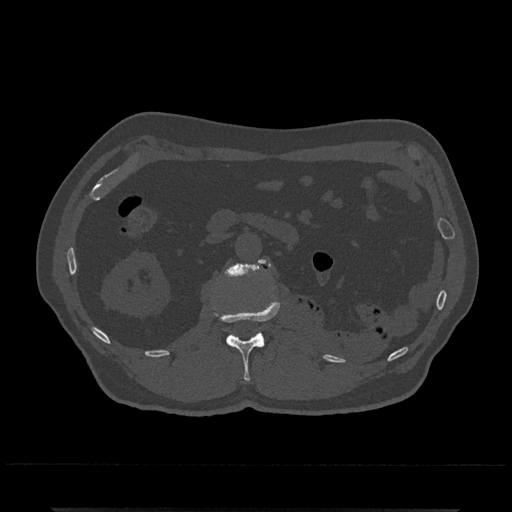
CT including the spine, one axial slice; position 340 of 797 along the scan axis; 120 kVp; bone window (W 1800 / L 400 HU); 0.5 mm slice thickness; 512 × 512 image matrix, field of view 393 × 393 mm. Patient: male, 67 years. Case-level facts recorded for this patient, not image findings: primary cancer: prostate.
Structures marked on this image (semi-automatically segmented with operator editing):
- L1 vertebra: box from (x=214, y=301) to (x=280, y=381) px
- L2 vertebra: (x=225, y=259)–(x=270, y=277)